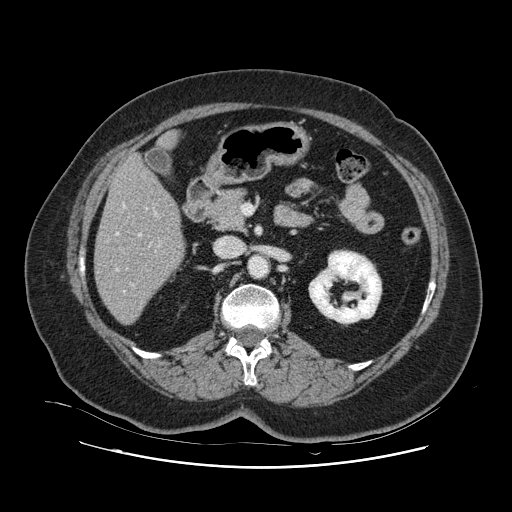
Contrast-enhanced abdominal CT, one axial slice. Slice 43 of 132 in the series (ordered by position). Intravenous contrast given. Soft-tissue window (W 400 / L 40 HU). 2.5 mm slice thickness. 512 × 512 image matrix, field of view 391 × 391 mm. Female patient, age 73 years. Case-level facts recorded for this patient, not image findings: diagnosis: colorectal cancer liver metastases, imaged before liver resection.
Outlined on this slice (outlined manually by an expert reader):
- hepatic veins: bounding box <116,204,157,293> (left, top, right, bottom; pixels)
- liver: <96,157,184,323>
- planned liver remnant (the part of the liver to remain after resection): <96,157,183,323>
- portal vein (with intrahepatic branches): <130,233,151,286>